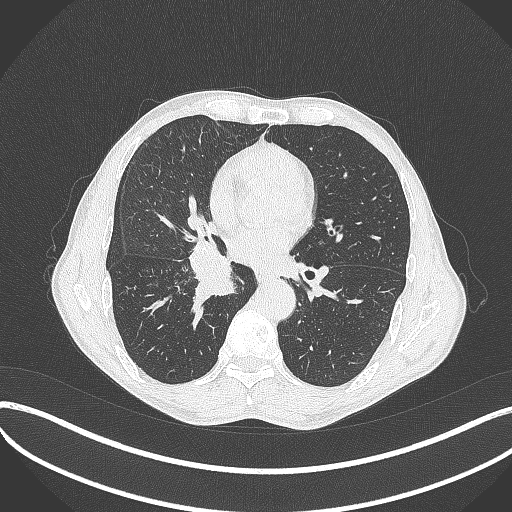
Chest CT, one axial slice; position 208 of 481 along the scan axis; lung window (W 1500 / L -600 HU); 1 mm slice thickness; 512 × 512 image matrix, field of view 400 × 400 mm. Male patient, age 65 years. Case-level facts recorded for this patient, not image findings: clinical TNM (as recorded): T2a N0 M0.
Annotated regions visible in this slice (rectangle marked by the reading radiologist):
- lung tumour (recorded histology: squamous cell carcinoma): bounding box (x1, y1, x2, y2) in pixels: (183, 239, 243, 307)